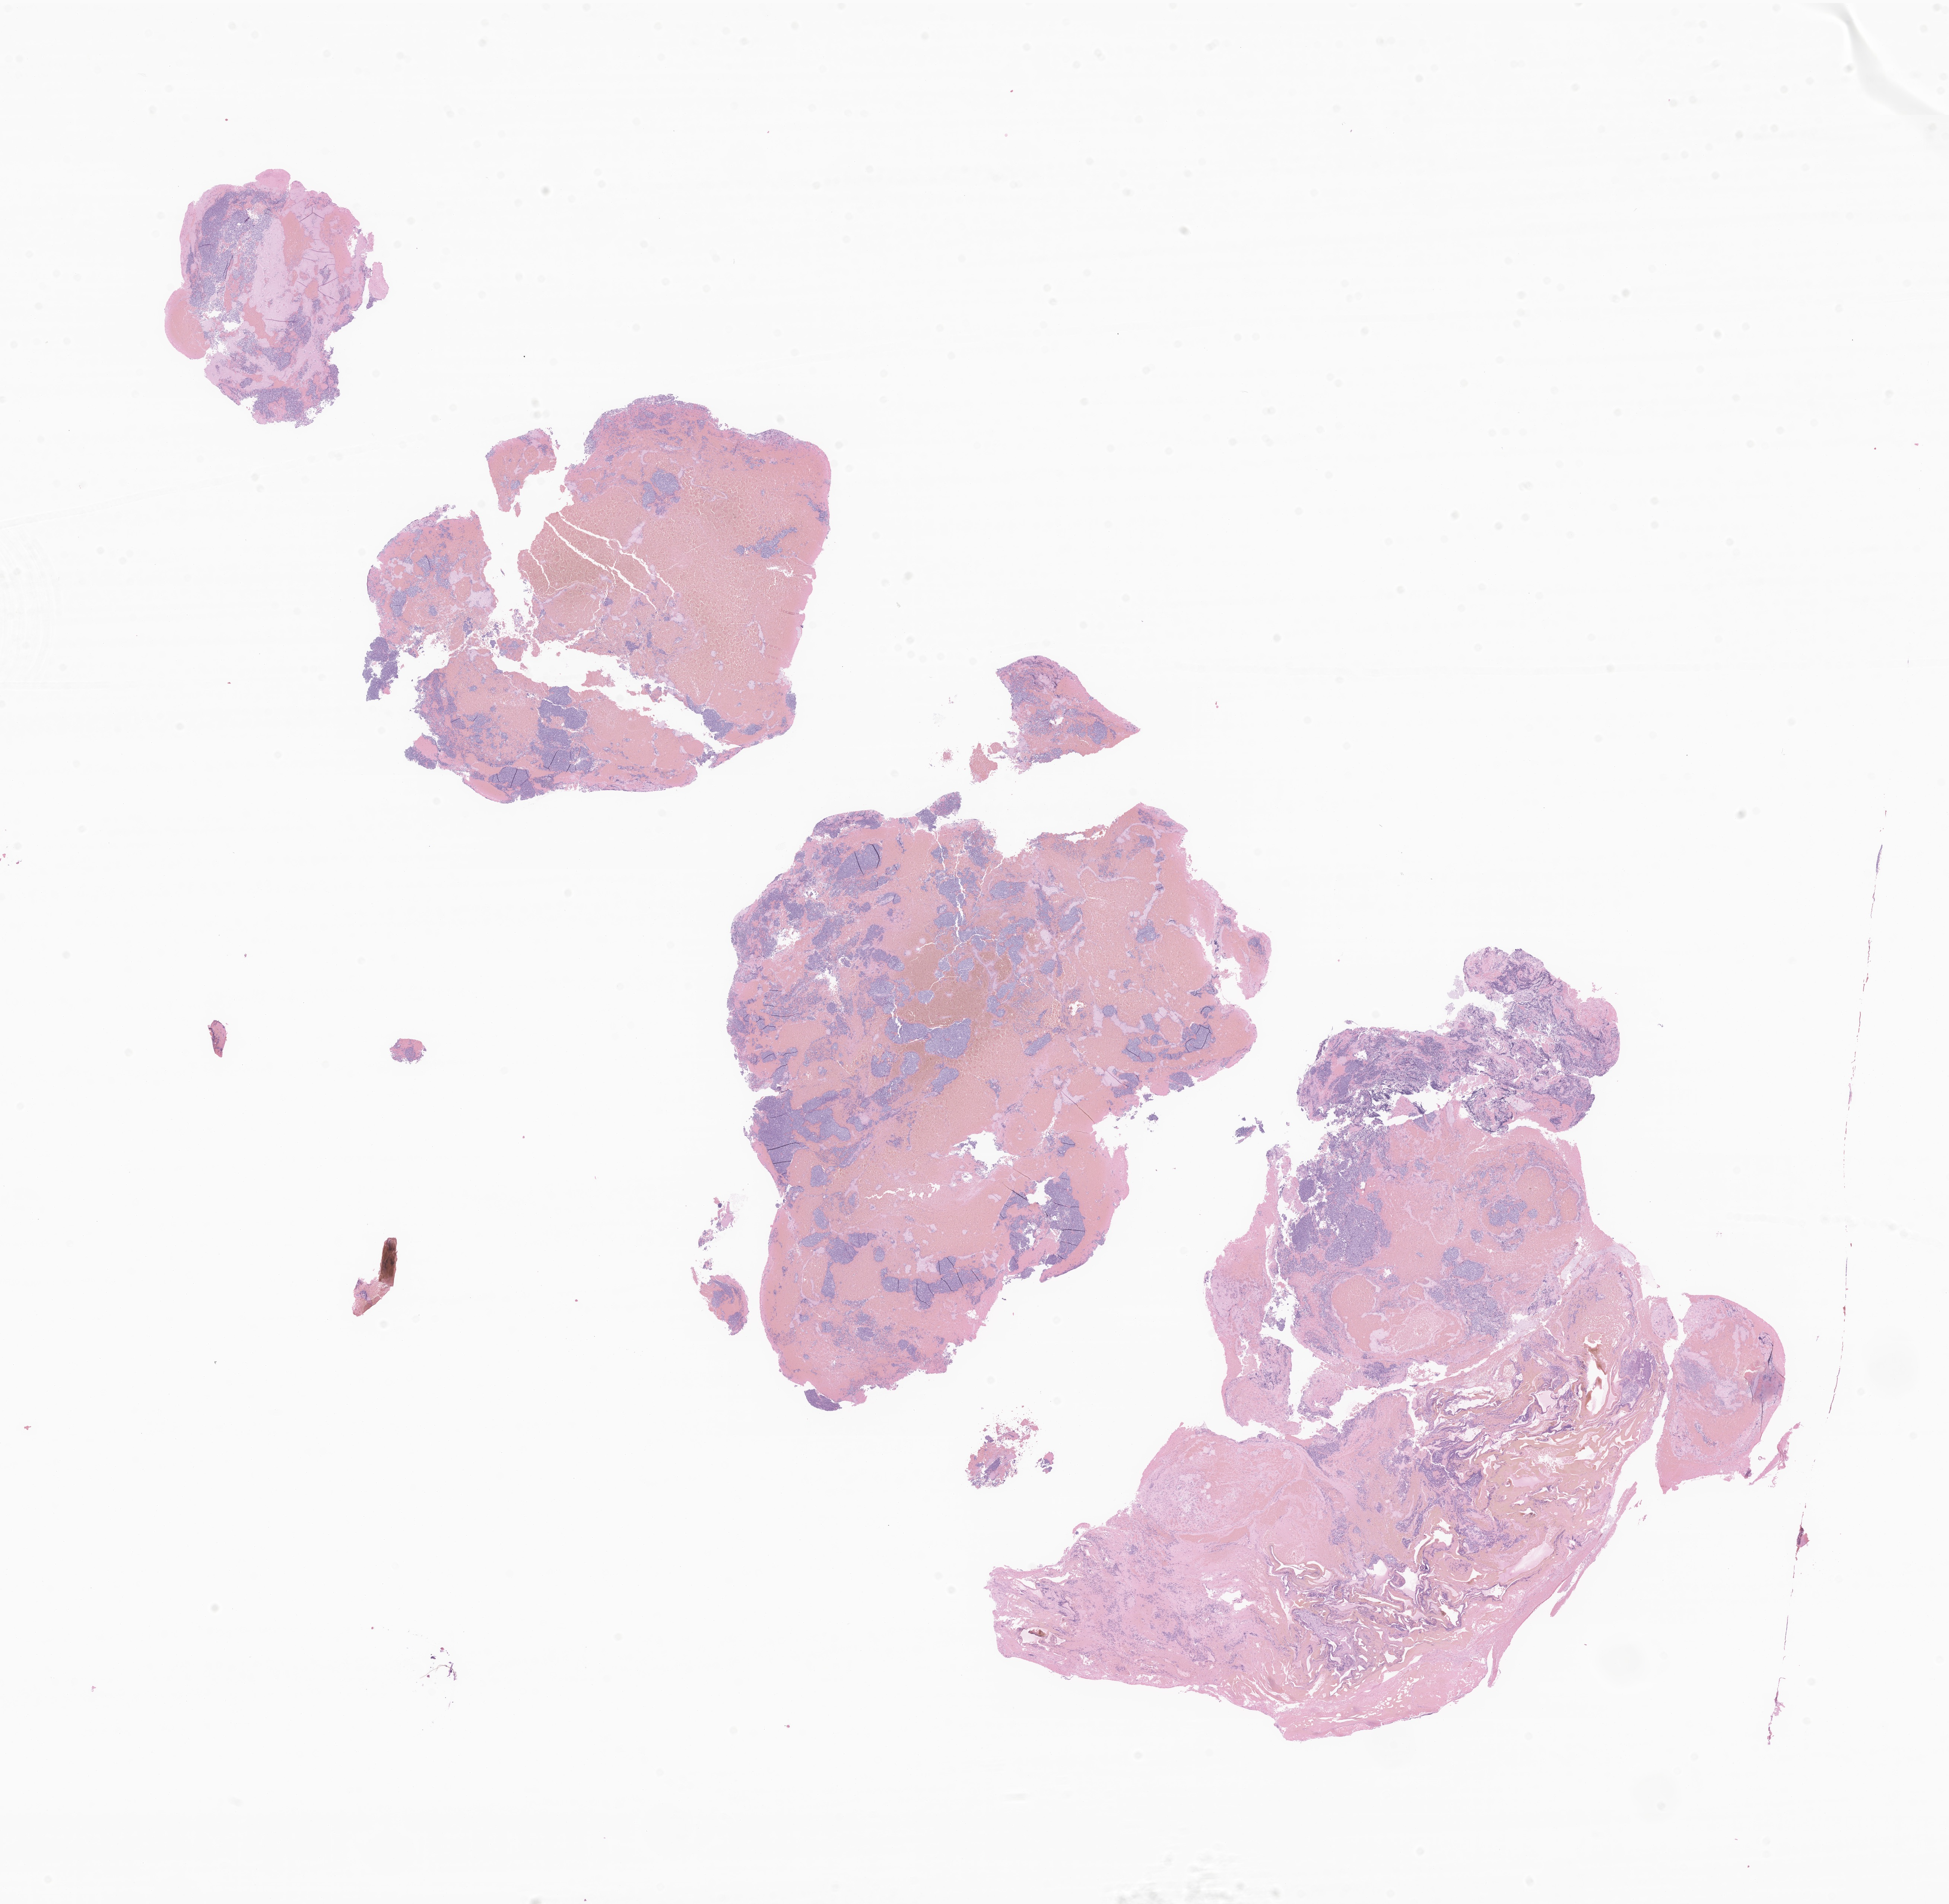
Whole-slide image, haematoxylin and eosin stain of tumor tissue from the cerebellum — shown as a low-resolution overview of the whole scanned area (about 22.1 x 21.5 mm), formalin-fixed paraffin-embedded section. Patient female; age 198 months (16 years 6 months).
Diagnosis (ICD-O-3 morphology term): Medulloblastoma, NOS.